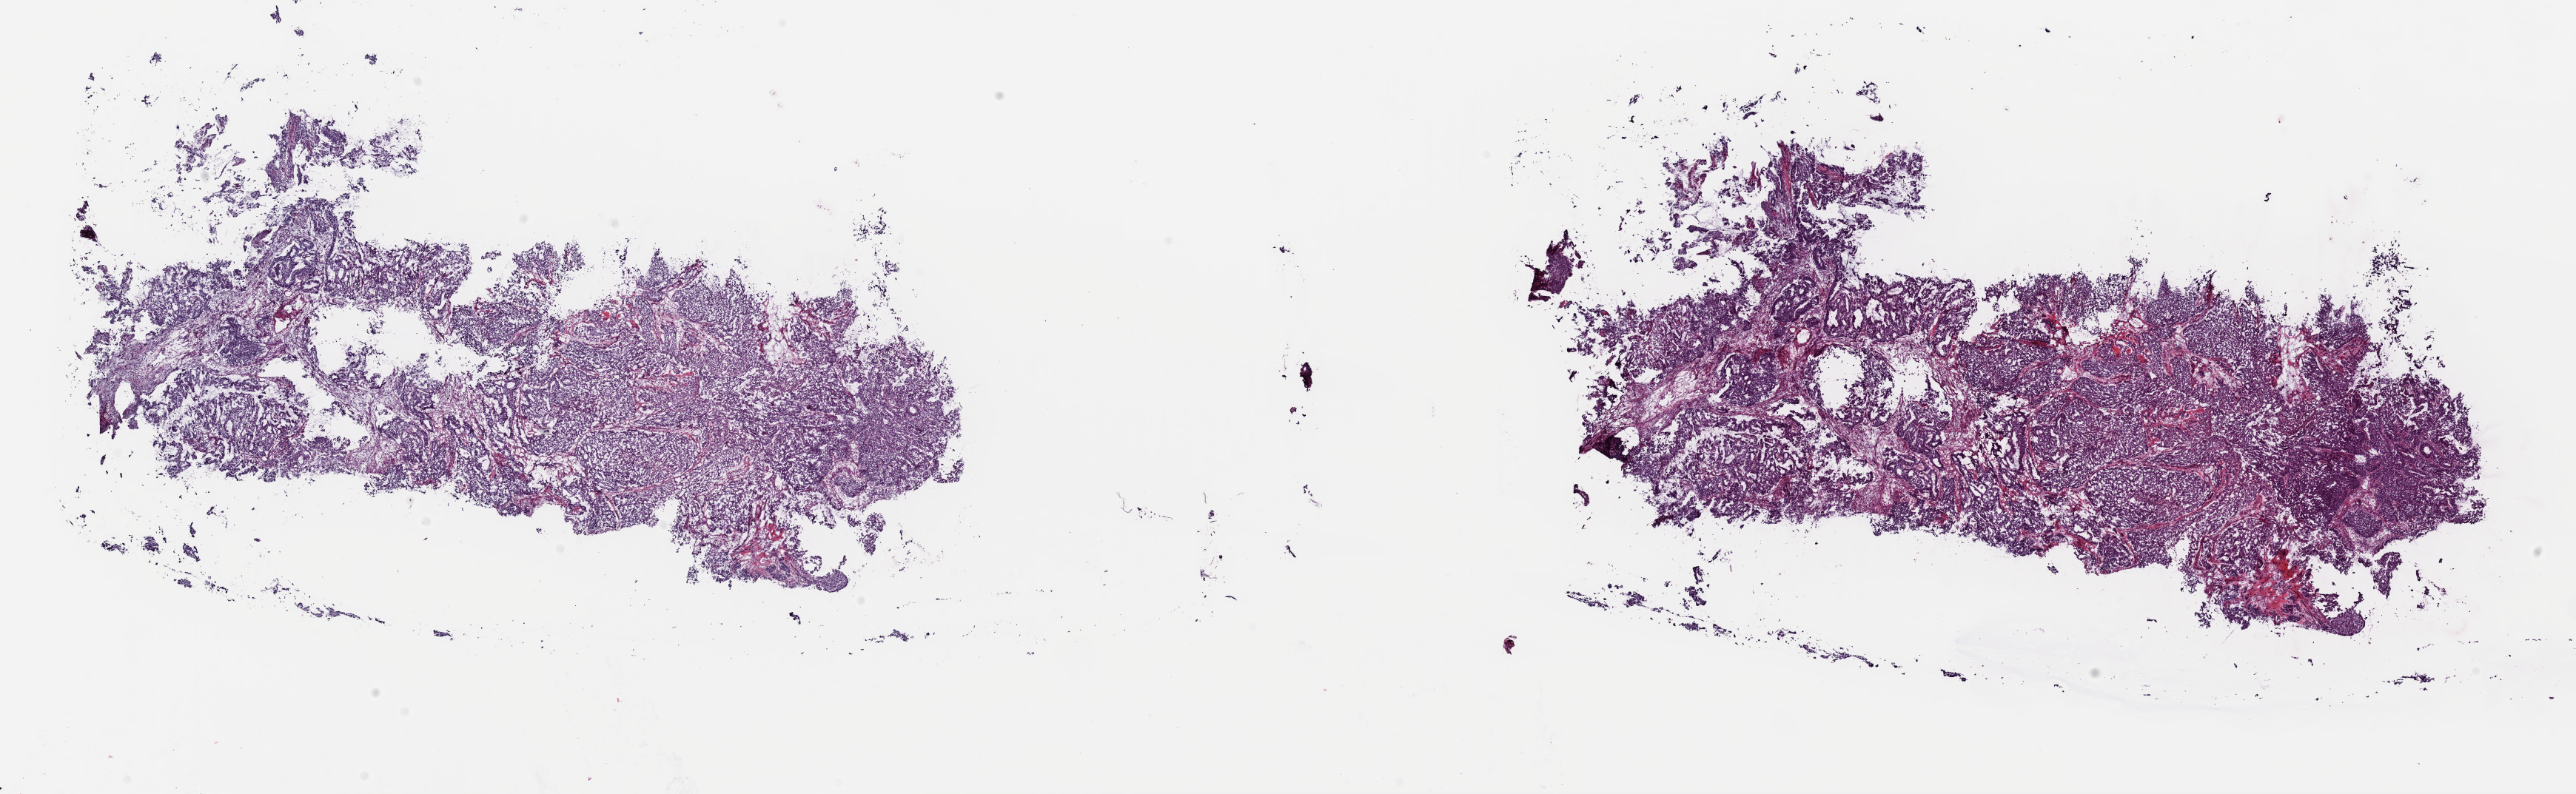
Whole-slide histology image, Hematoxylin and eosin (H&E) stained — a low-resolution overview of the entire scanned area, about 27.5 x 8.5 mm, frozen section from the top of the tissue portion, uterus, primary tumour sample. Female patient; age at initial diagnosis 62 years. Histologic grade: G3 (poorly differentiated). Slide review estimates, as recorded: tumour cells 80%, tumour nuclei 85%, normal cells 5%, stromal cells 15%, necrosis 0%. Inflammatory infiltration, as recorded: lymphocyte infiltration 2%, monocyte infiltration 0%, neutrophil infiltration 0%.
FIGO stage: III. Histologic diagnosis: Endometrioid adenocarcinoma, NOS.